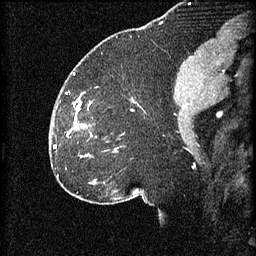
Breast MRI (dynamic contrast-enhanced), one sagittal slice; slice 33 of 60 in the series (ordered by position); 3 images stored at this slice position (order not interpretable as contrast timing); 1.5 T; TE 4.2 ms, TR 8.2 ms; 2 mm slice thickness; 256 × 256 image matrix, field of view 180 × 180 mm. Patient: female, 32 years.
Structures marked on this image (semi-automatic segmentation, software-assisted and operator-edited):
- analysis volume of interest (the breast-tissue region the enhancement analysis was run in; not a lesion): box from (x=68, y=106) to (x=92, y=157) px
- tumour enhancement mask (voxels above the 70 % enhancement threshold inside the analysis volume of interest): (x=76, y=126)–(x=78, y=129)